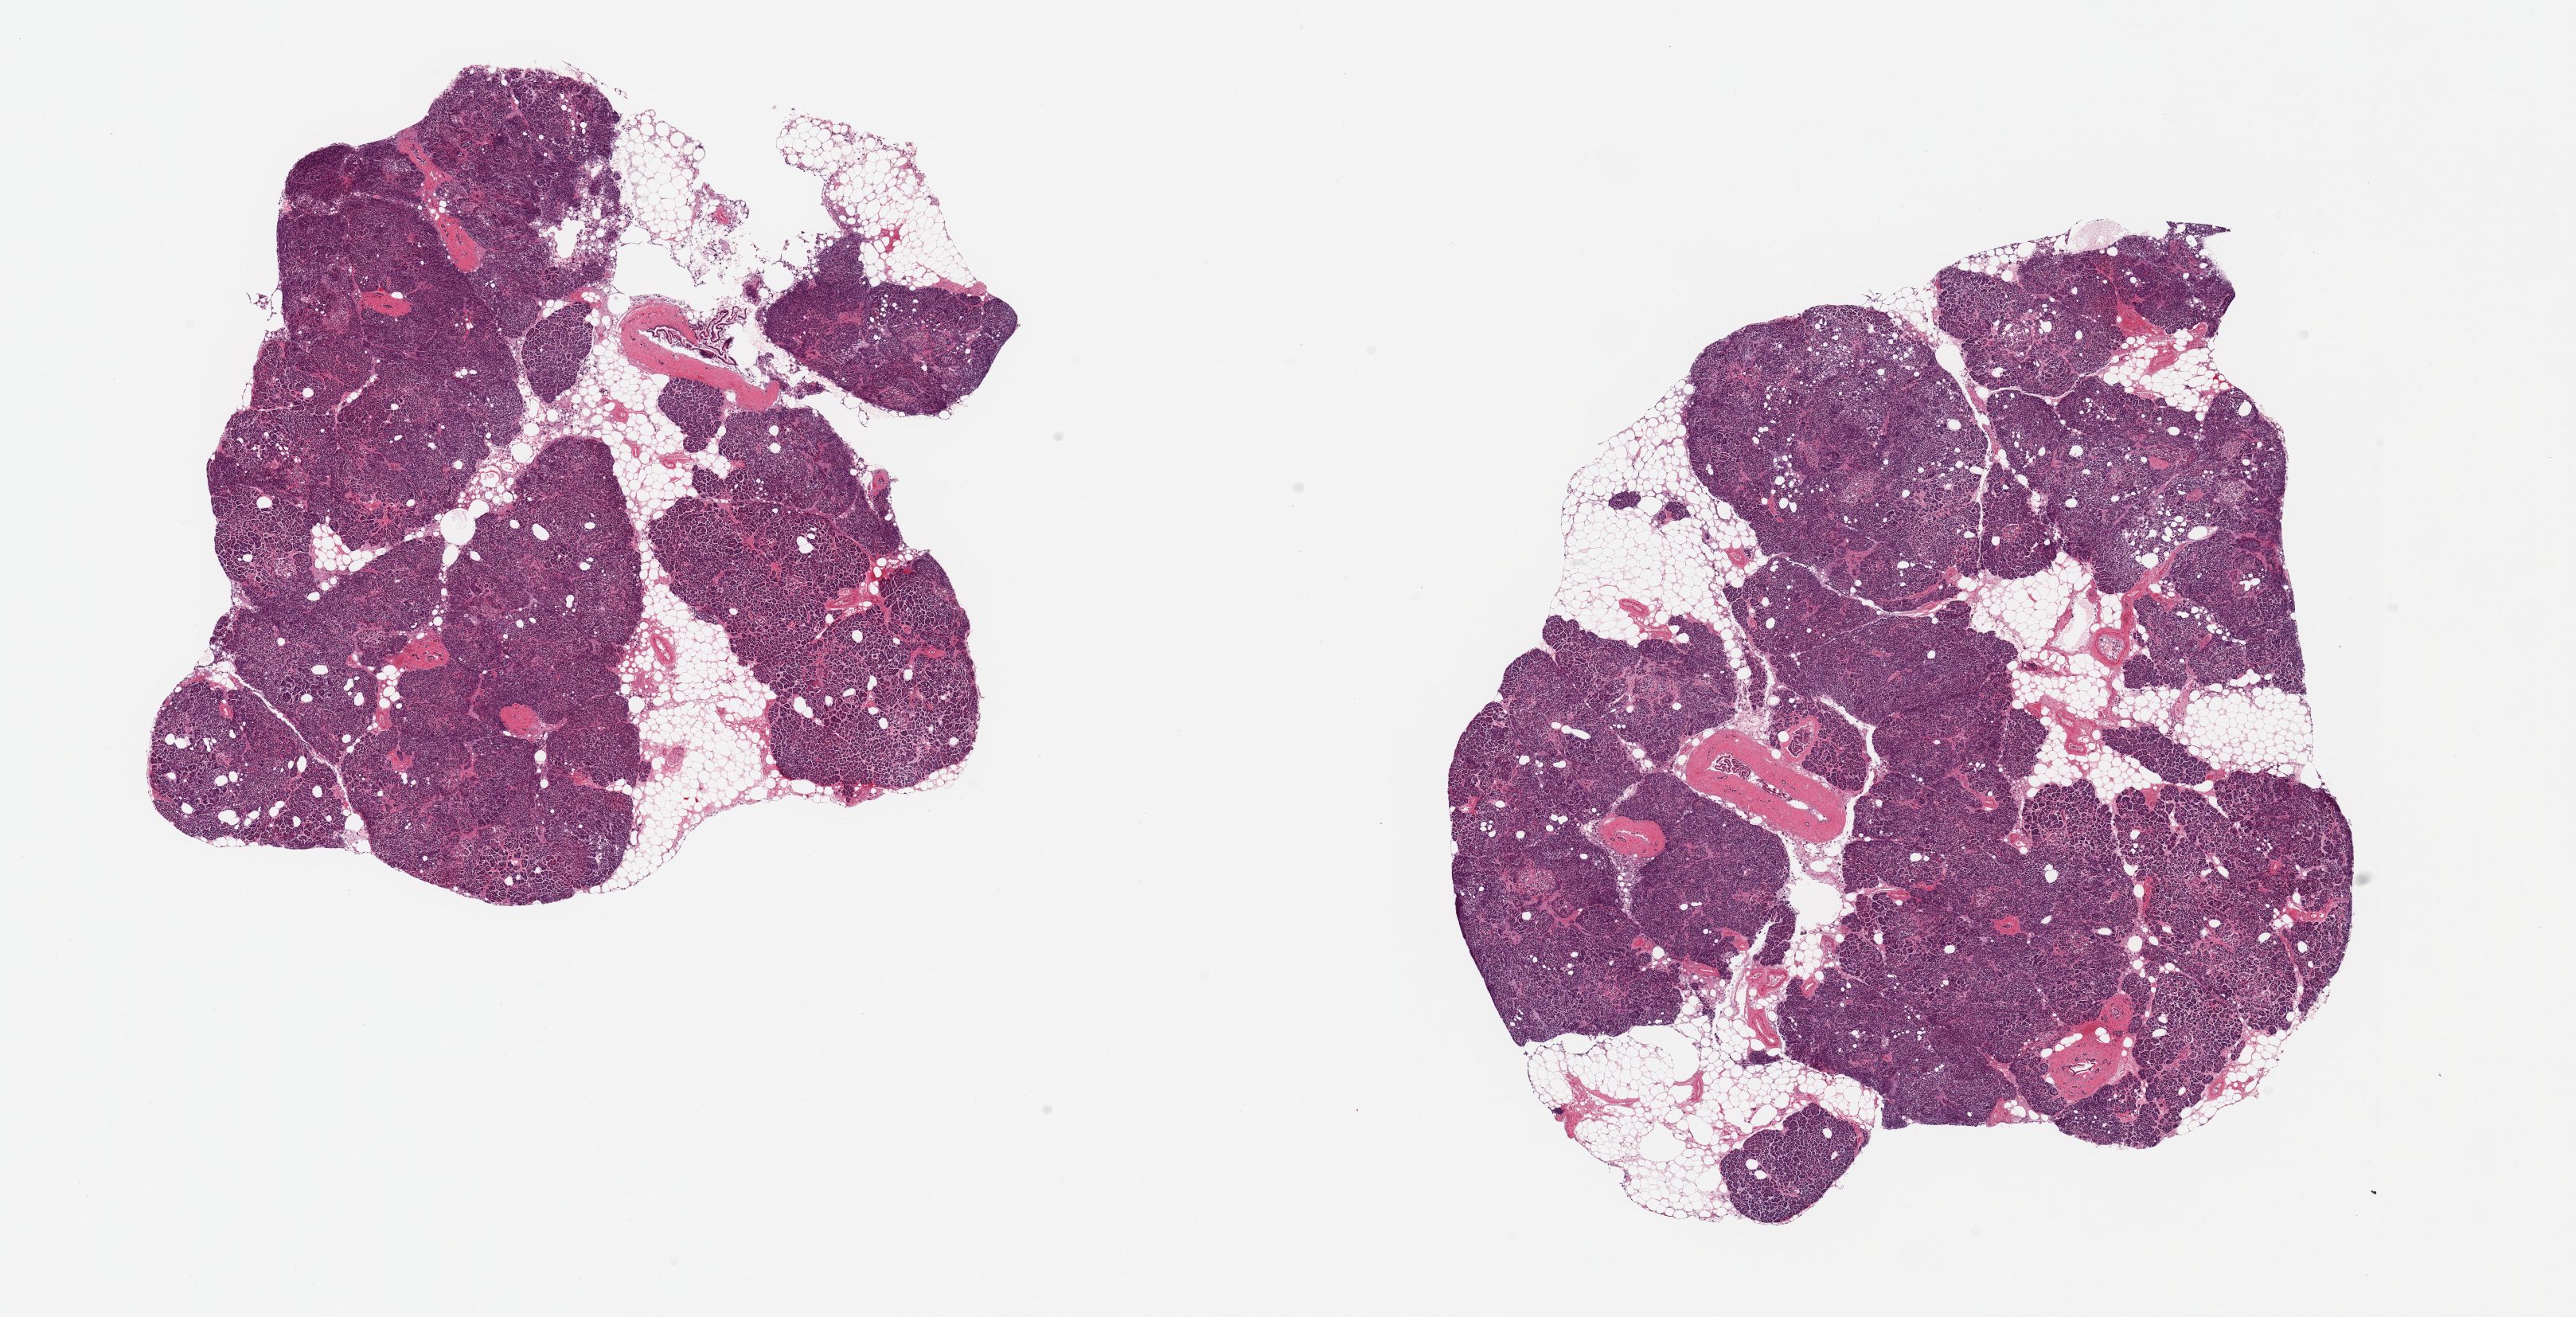
Whole-slide image, H&E stain, brightfield — whole scanned area (about 25.6 x 13.1 mm, acquisition: 20x scan) shown as a low-resolution overview, PAXgene-fixed, paraffin-embedded tissue, target tissue: pancreas, tissue donor sample. Female donor.
Pathologist's review note for this sample: 2 pieces; 20% internal fat.